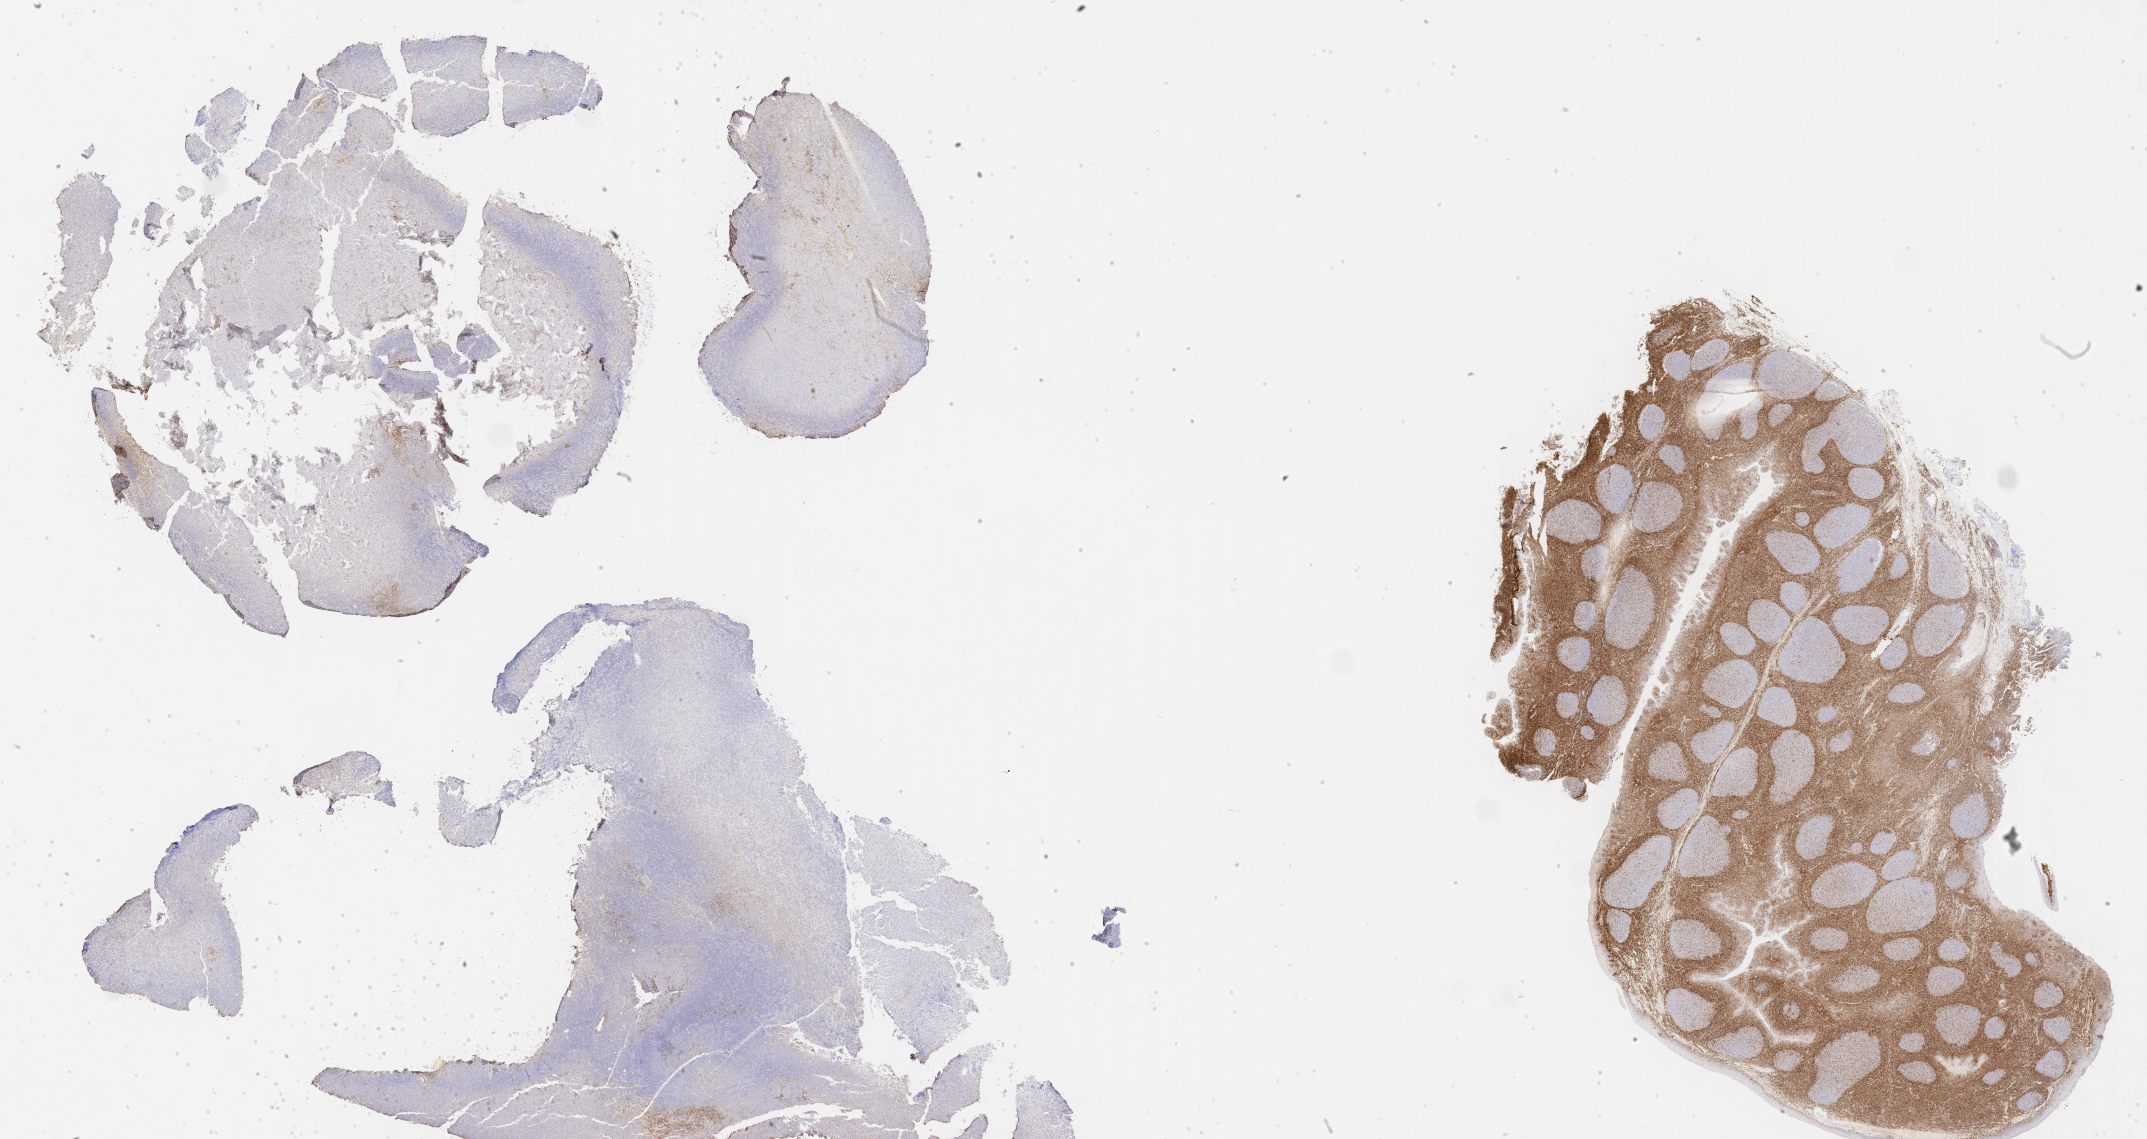
Whole-slide image, immunohistochemical stain for BCL2, low-resolution overview of the scanned area, about 34.7 x 18.4 mm; specimen: tumor tissue; anatomic site: liver. Patient: male, age 45 years.
Histologic diagnosis: Diffuse large B-cell lymphoma, NOS.